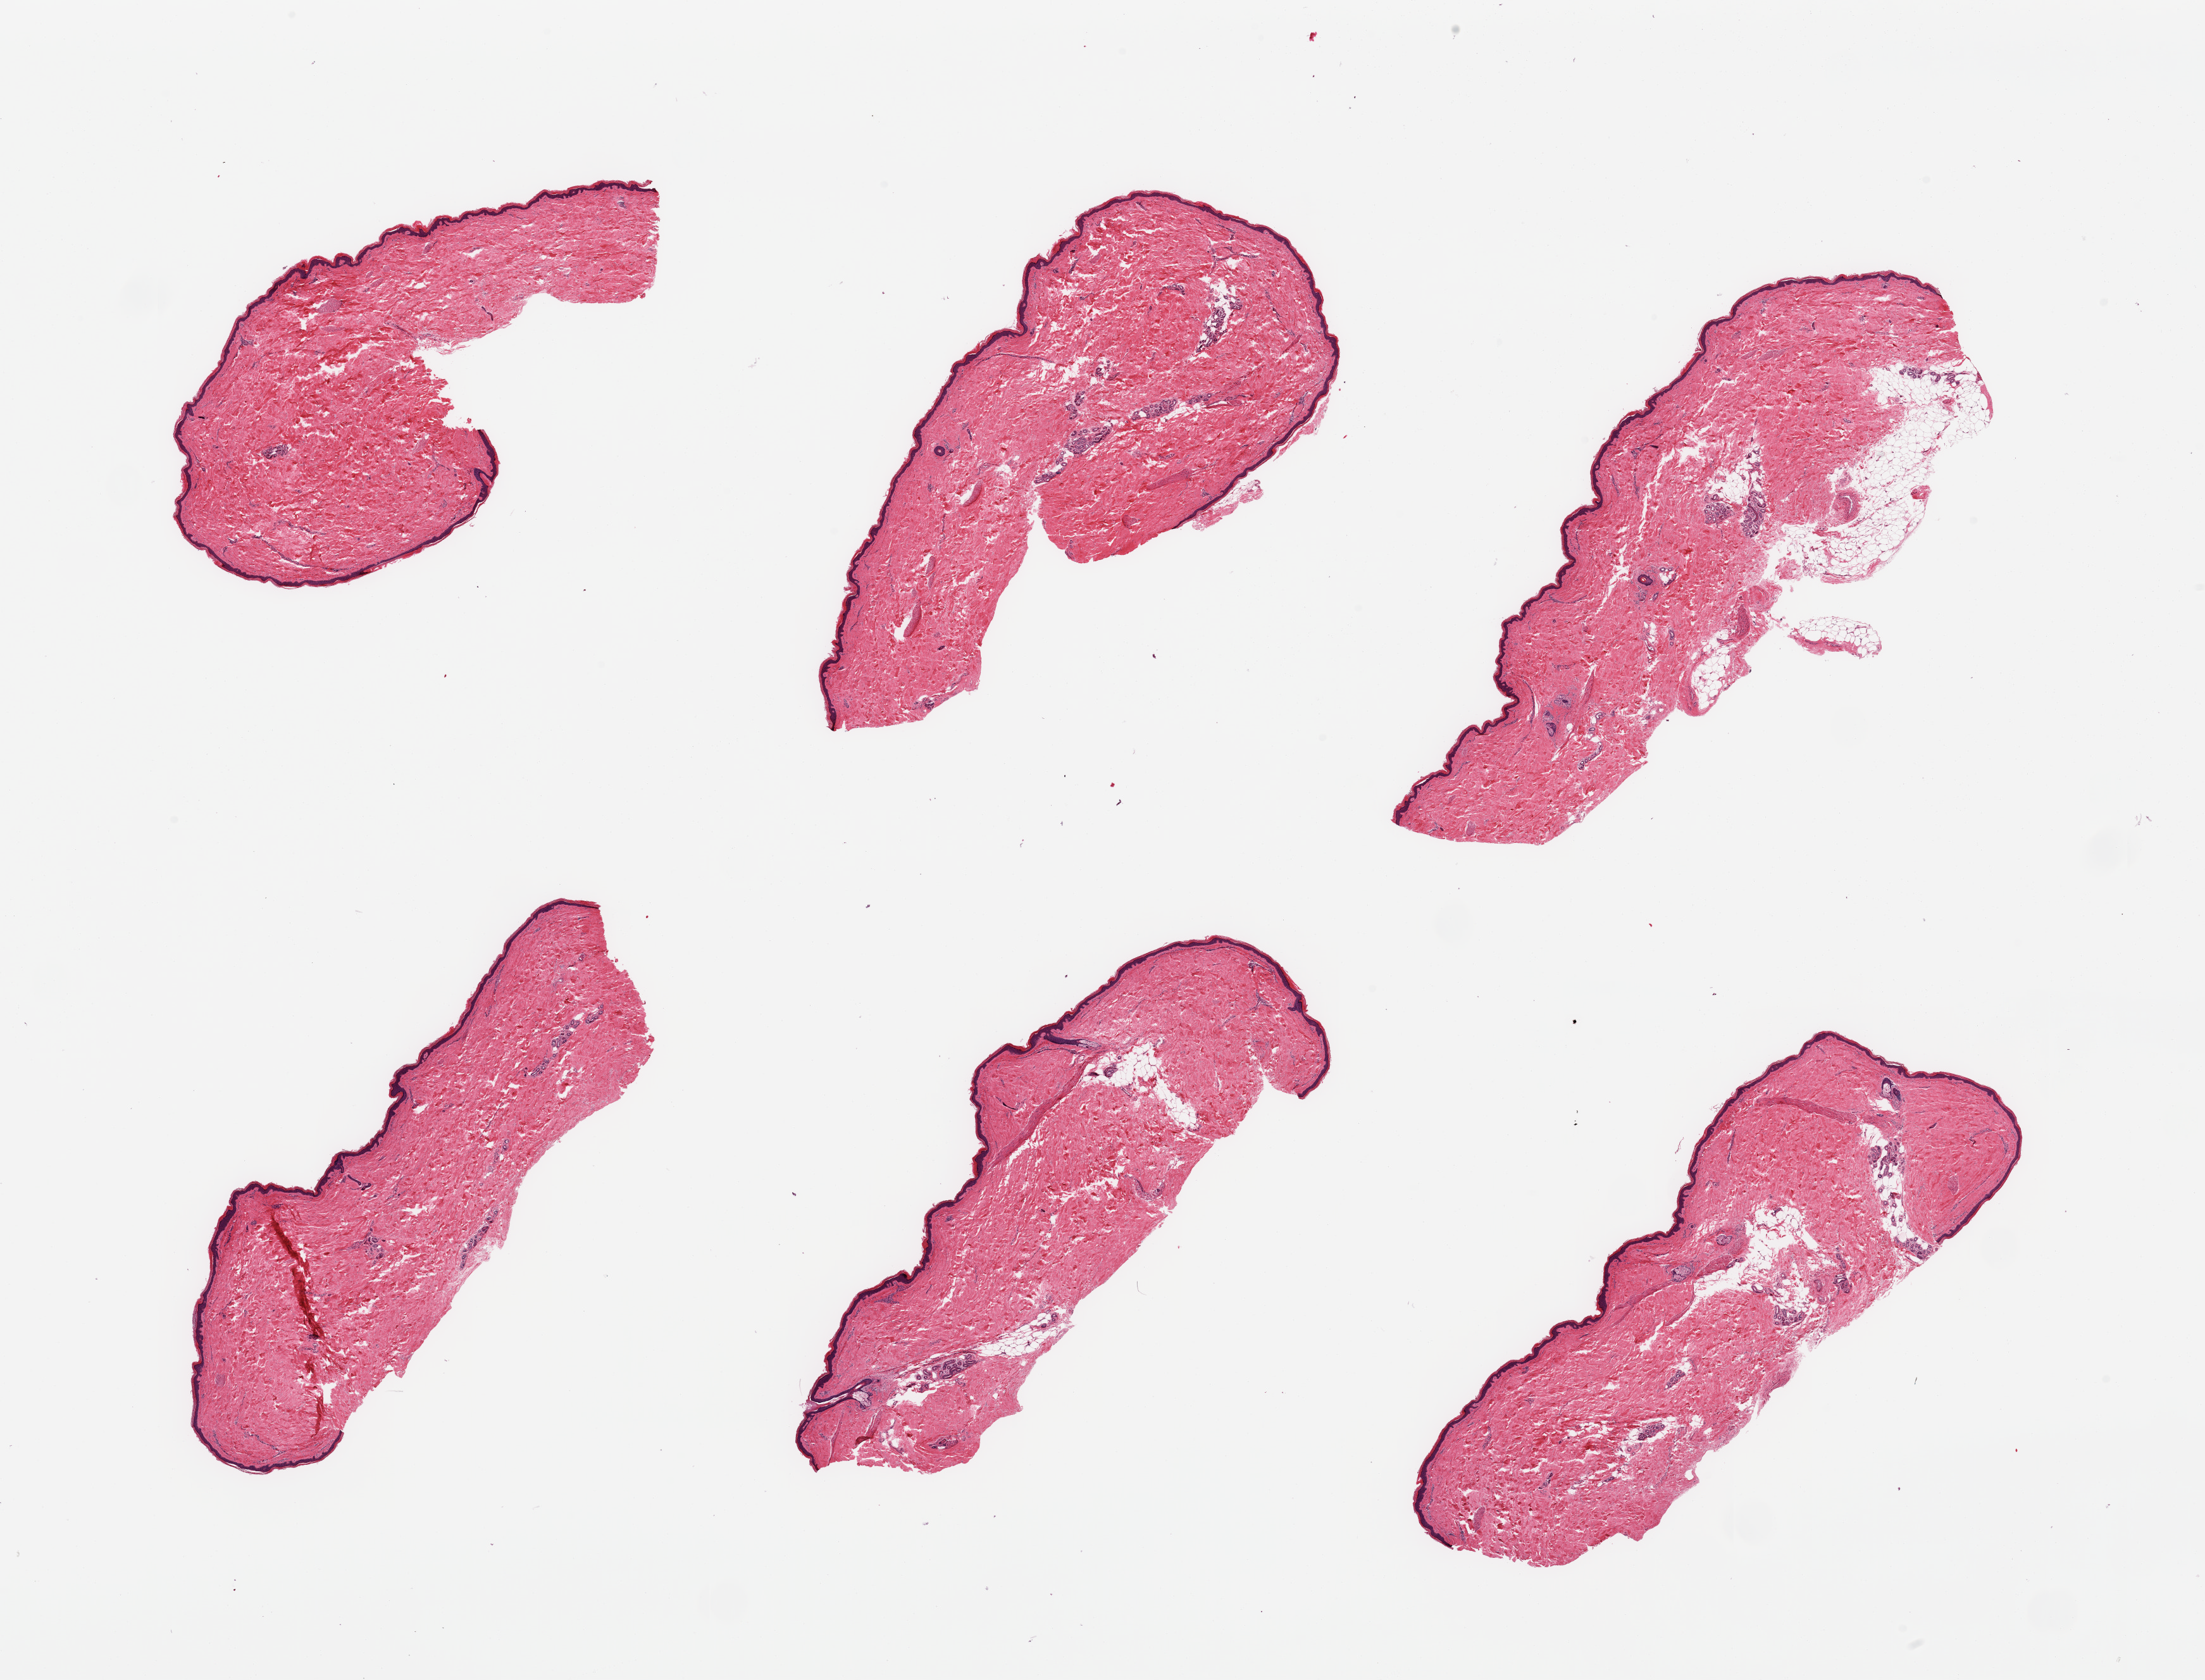
Digitized hematoxylin and eosin (H&E)-stained section — shown as a low-resolution overview of the whole scanned area (about 27.6 x 21.0 mm, acquisition: 20x scan); PAXgene-fixed paraffin-embedded (PFPE) section; section of skin of lower leg (target tissue); donor tissue sample.
Pathologist's review note for this sample: 6 pieces; 0 to 10% internal (periadnexal fat) and one piece with ~20% external fat; ~36 micron thick epidermis.